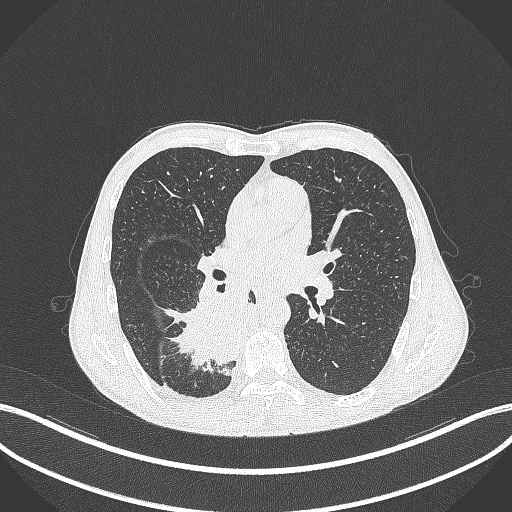
Chest CT, one axial slice; position 197 of 371 along the scan axis; 120 kVp; lung window (W 1500 / L -600 HU); 512 × 512 image matrix, field of view 400 × 400 mm. Patient: male, 58 years. Case-level facts recorded for this patient, not image findings: clinical TNM (as recorded): T3 N1 M1.
Outlined on this slice (bounding box drawn by a radiologist):
- lung tumour (recorded histology: squamous cell carcinoma): bounding box <160,281,263,385> (left, top, right, bottom; pixels)